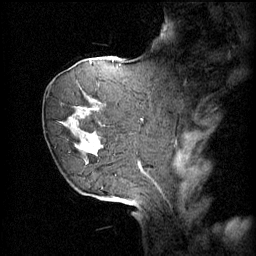
Breast MRI (dynamic contrast-enhanced), one sagittal slice; position 16 of 60 along the scan axis; 4 images stored at this slice position (order not interpretable as contrast timing); 1.5 T; TE 4.2 ms, TR 11 ms; 2 mm slice thickness; 256 × 256 image matrix, field of view 220 × 220 mm. Female patient, age 72 years.
Outlined on this slice (semi-automatically segmented with operator editing):
- analysis volume of interest (the breast-tissue region the enhancement analysis was run in; not a lesion): box from (x=54, y=68) to (x=109, y=163) px
- tumour enhancement mask (voxels above the 70 % enhancement threshold inside the analysis volume of interest): (x=68, y=100)–(x=109, y=151)